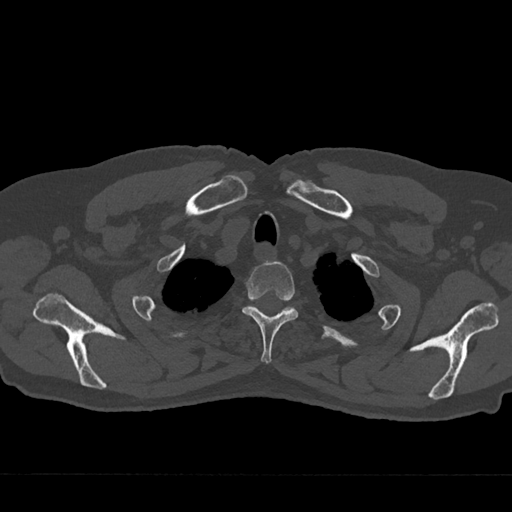
CT including the spine, one axial slice; position 608 of 797 along the scan axis; reconstruction kernel Br40s/3; 120 kVp; bone window (W 1800 / L 400 HU); 0.5 mm slice thickness; 512 × 512 image matrix, field of view 377 × 377 mm. Male patient, age 75 years. Case-level facts recorded for this patient, not image findings: primary cancer: renal.
Outlined on this slice (semi-automatic segmentation, software-assisted and operator-edited):
- T2 vertebra: box from (x=242, y=261) to (x=298, y=364) px
- T3 vertebra: (x=255, y=307)–(x=291, y=311)